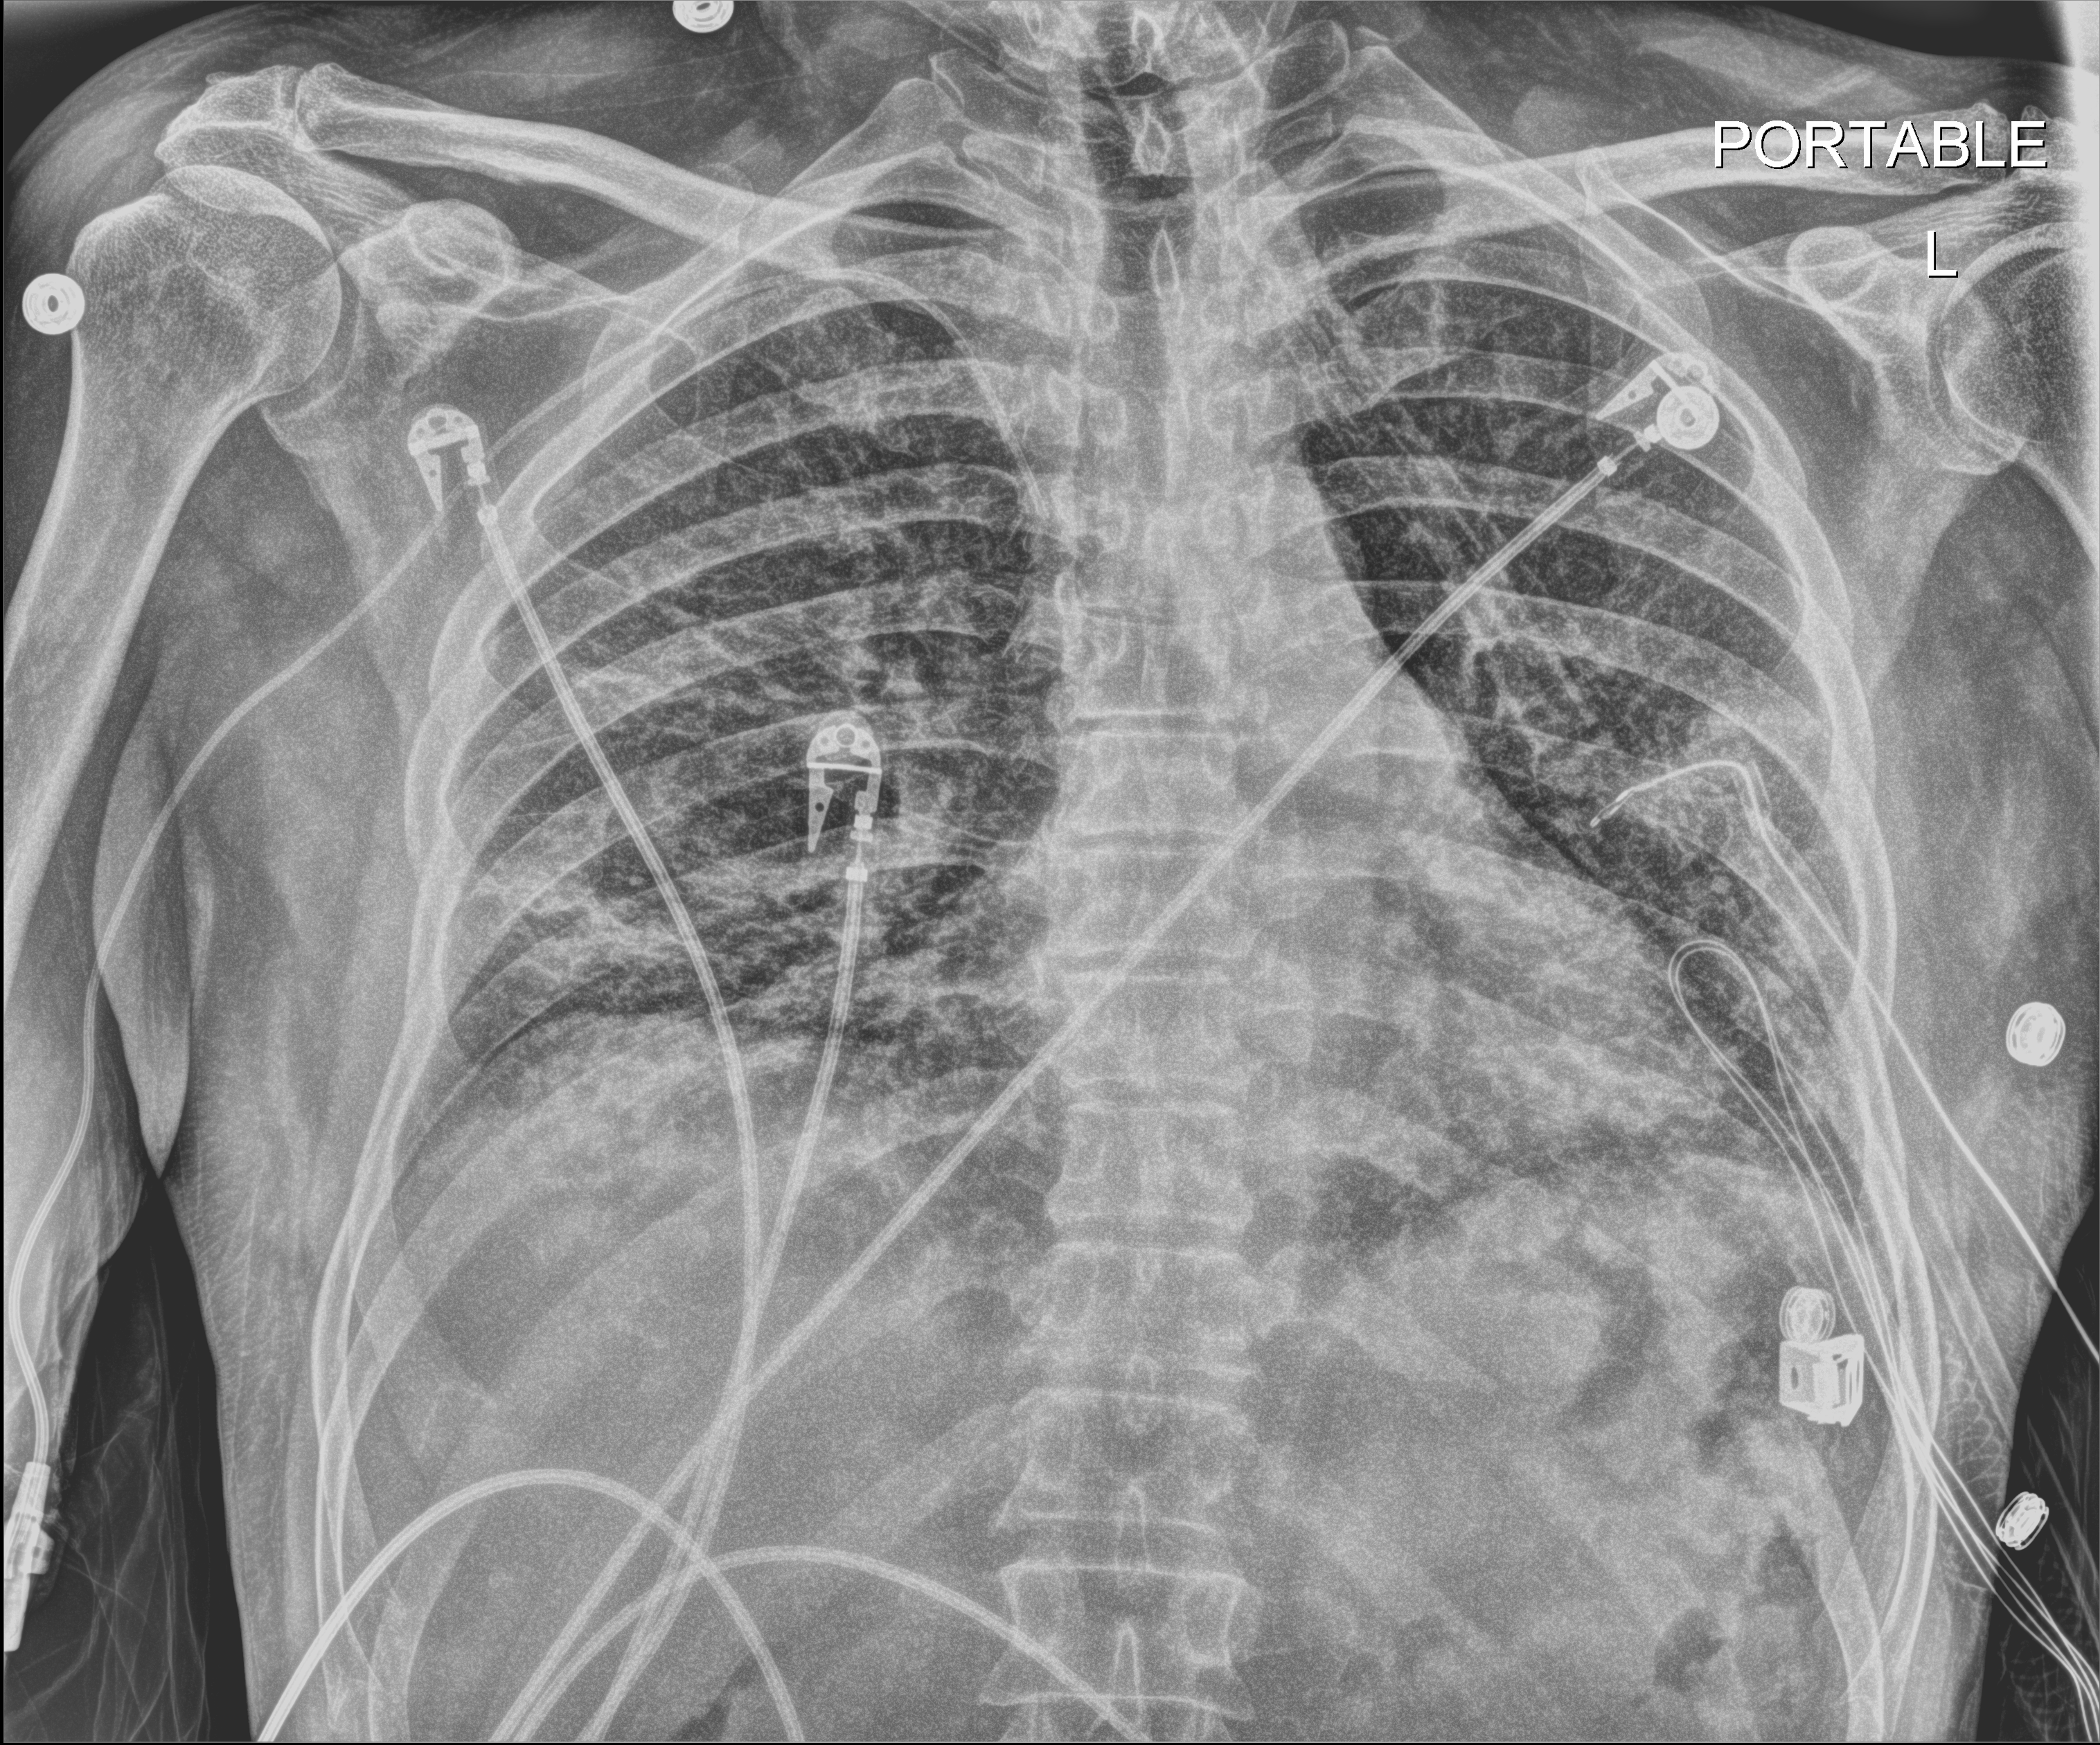
Chest X-ray (portable), anteroposterior (AP) projection. Male patient hospitalised with COVID-19, age 18–59 years.
From the hospital-stay record, not from the radiograph (when in the stay this image was taken is not recorded): length of hospital stay: 38 days; smoking status (admission record): never; mechanically ventilated during this hospital stay: no.